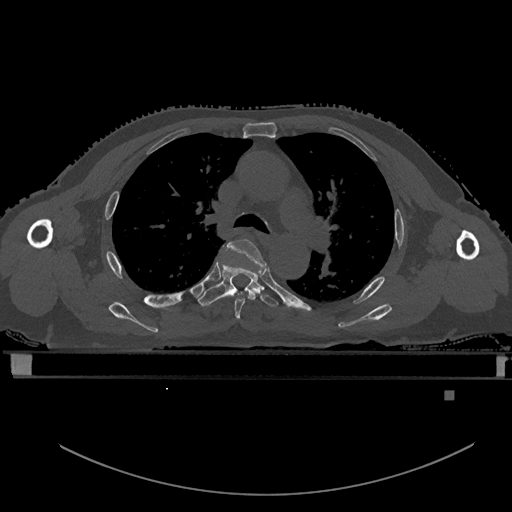
CT including the spine, one axial slice. Slice 378 of 969 in the series (ordered by position). Bone window (W 1800 / L 400 HU). 0.5 mm slice thickness. 512 × 512 image matrix. Patient: male, 82 years. From the clinical record (not read from this slice): primary cancer: prostate; vertebrae with lytic lesions (as recorded): T11, T9, T8, T2.
Structures marked on this image (semi-automatic segmentation, software-assisted and operator-edited):
- T4 vertebra: bounding box (x1, y1, x2, y2) in pixels: (223, 239, 266, 319)
- T5 vertebra: (198, 254, 278, 307)